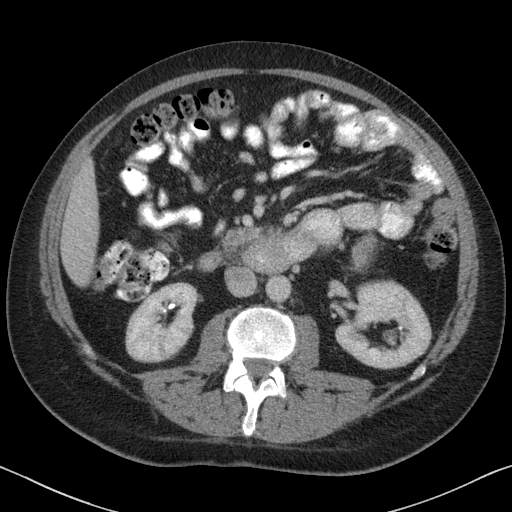
Contrast-enhanced abdominal CT, one axial slice; slice 30 of 88 in the series (ordered by position); reconstruction kernel B31f; intravenous contrast given; soft-tissue window (W 400 / L 40 HU); 3 mm slice thickness; 512 × 512 image matrix. Male patient, age 51 years. Case-level facts recorded for this patient, not image findings: diagnosis: adrenocortical carcinoma; tumour side: left adrenal; tumour size at pathology: 16.5 cm; Ki-67 index: 30 %; stage (as recorded): 2.
Outlined on this slice (semi-automatically segmented with operator editing):
- mass: bounding box <351,238,378,270> (left, top, right, bottom; pixels)